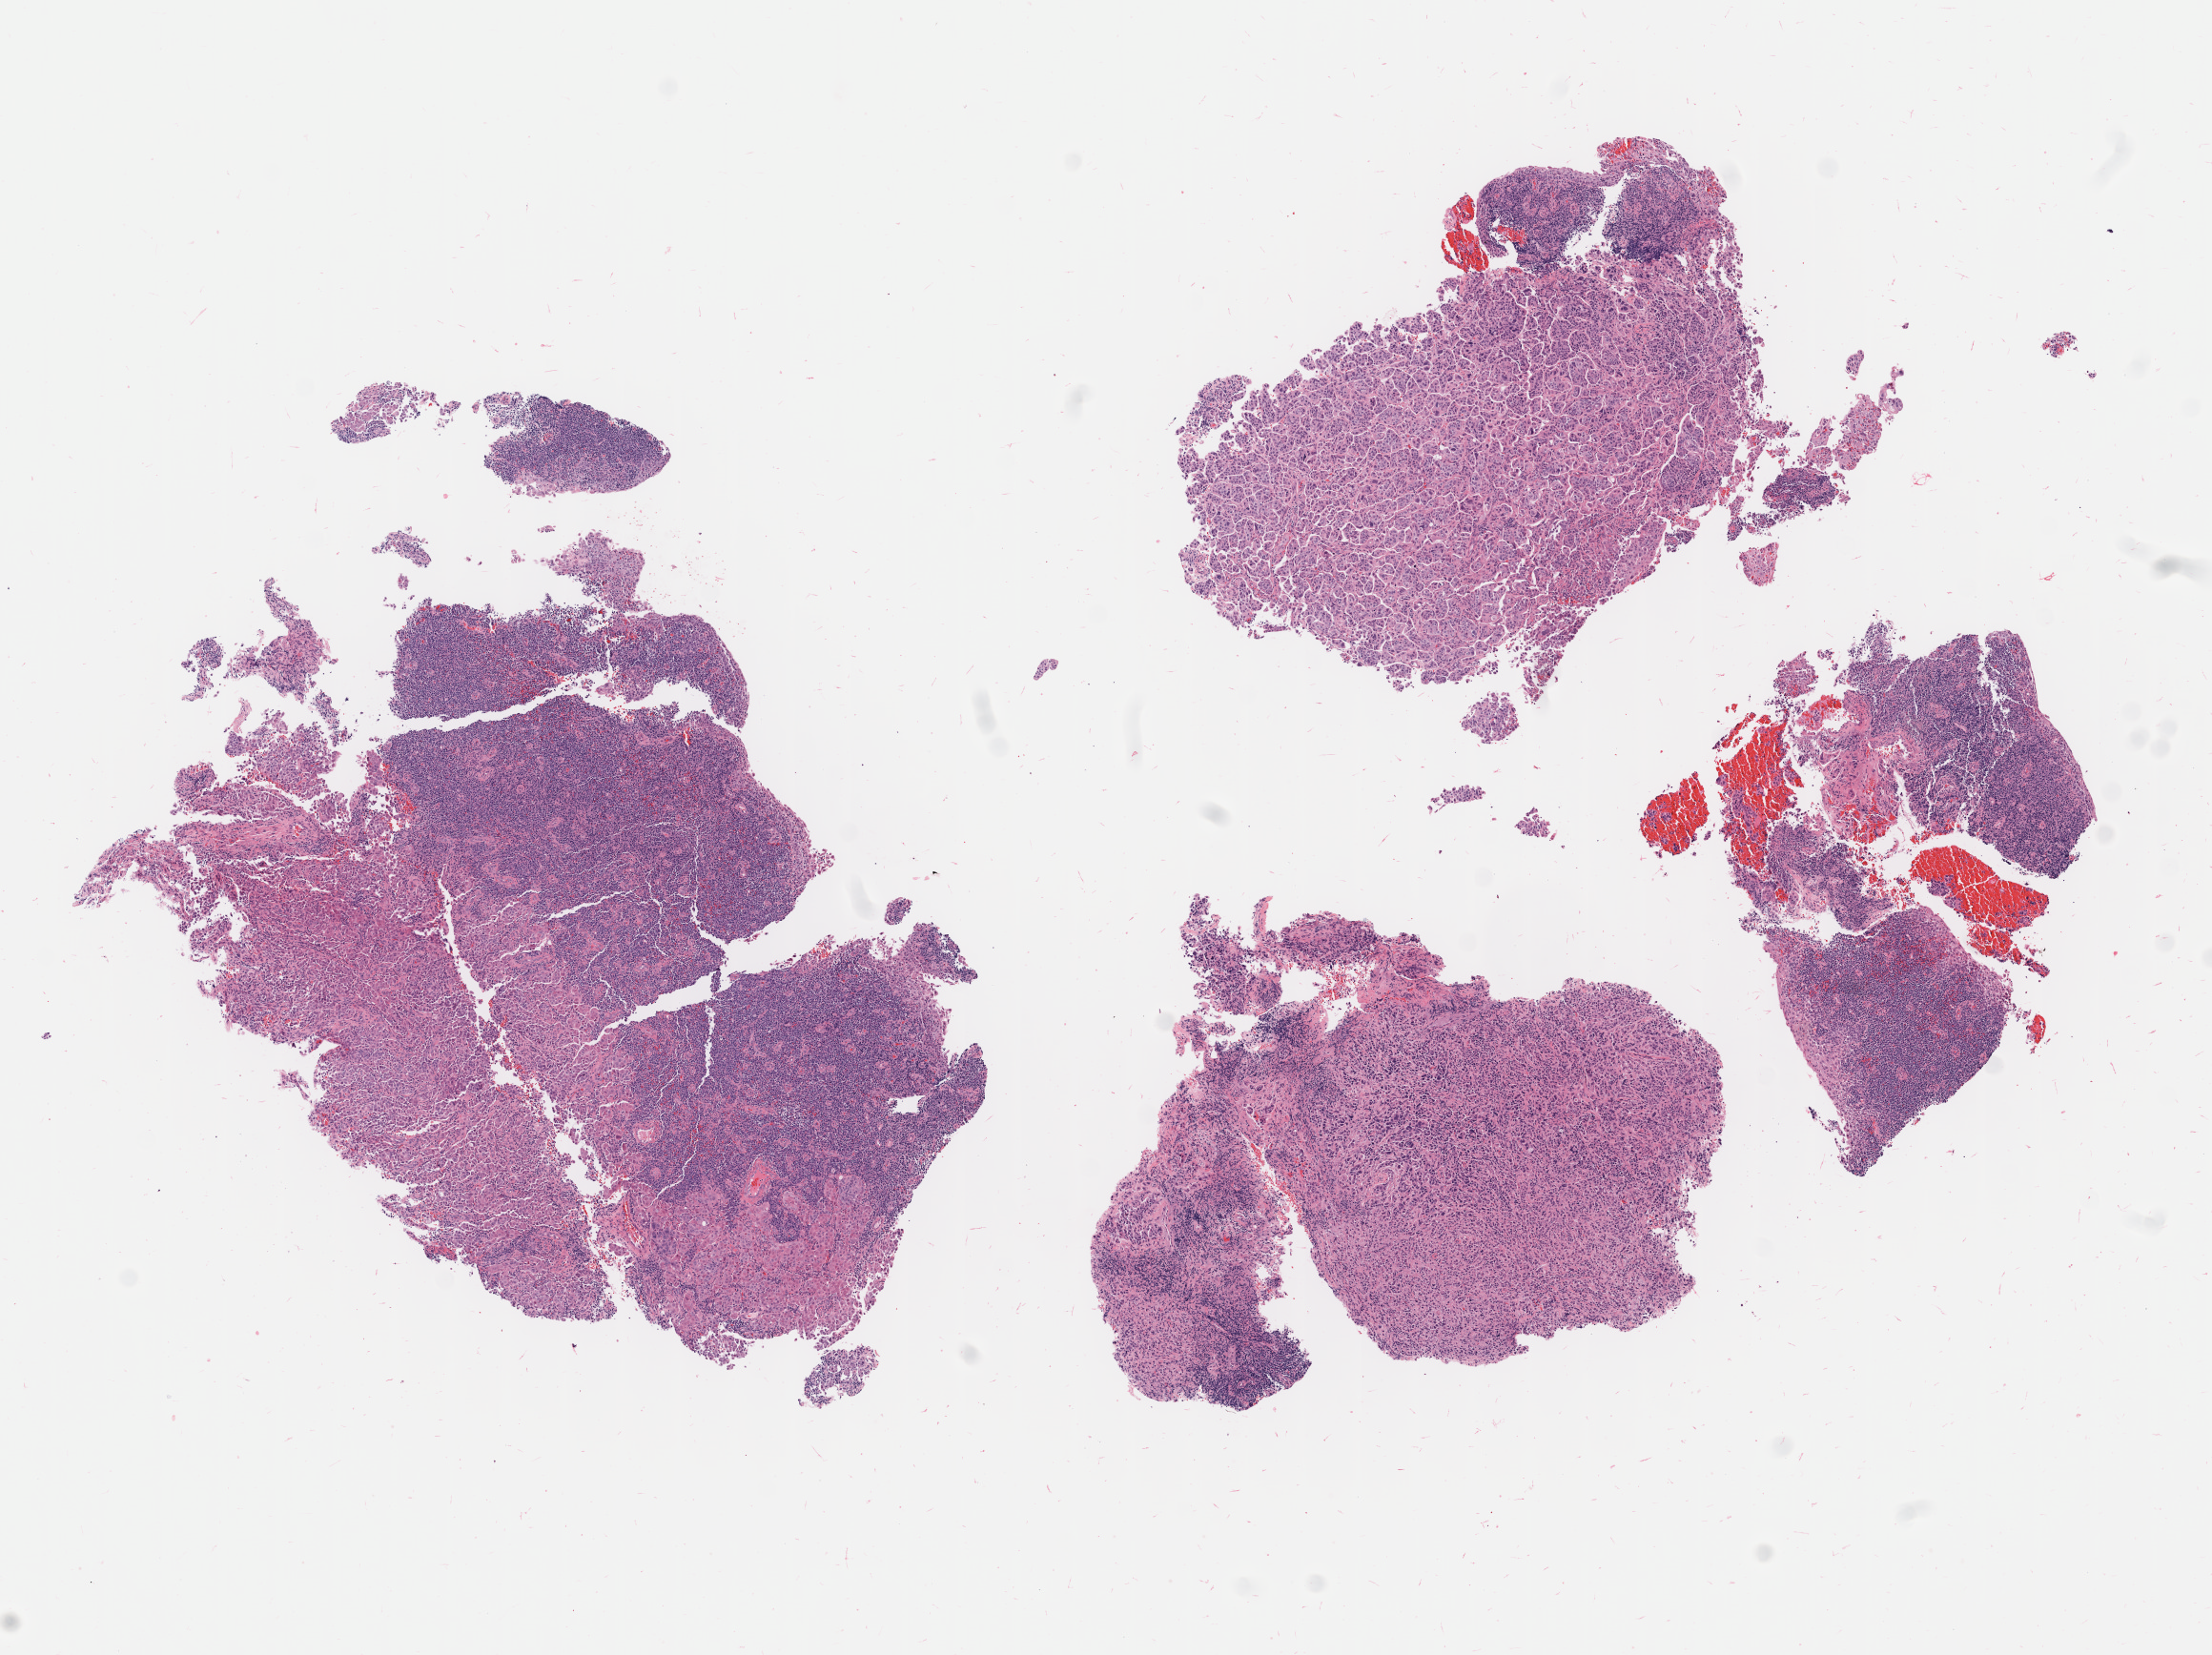
Whole-slide image, H&E stain — low-resolution overview of the scanned area, about 9.2 x 6.9 mm; specimen: tumor tissue; site: cervix. Patient: female, aged 54.
• diagnosis: Adenocarcinoma, NOS